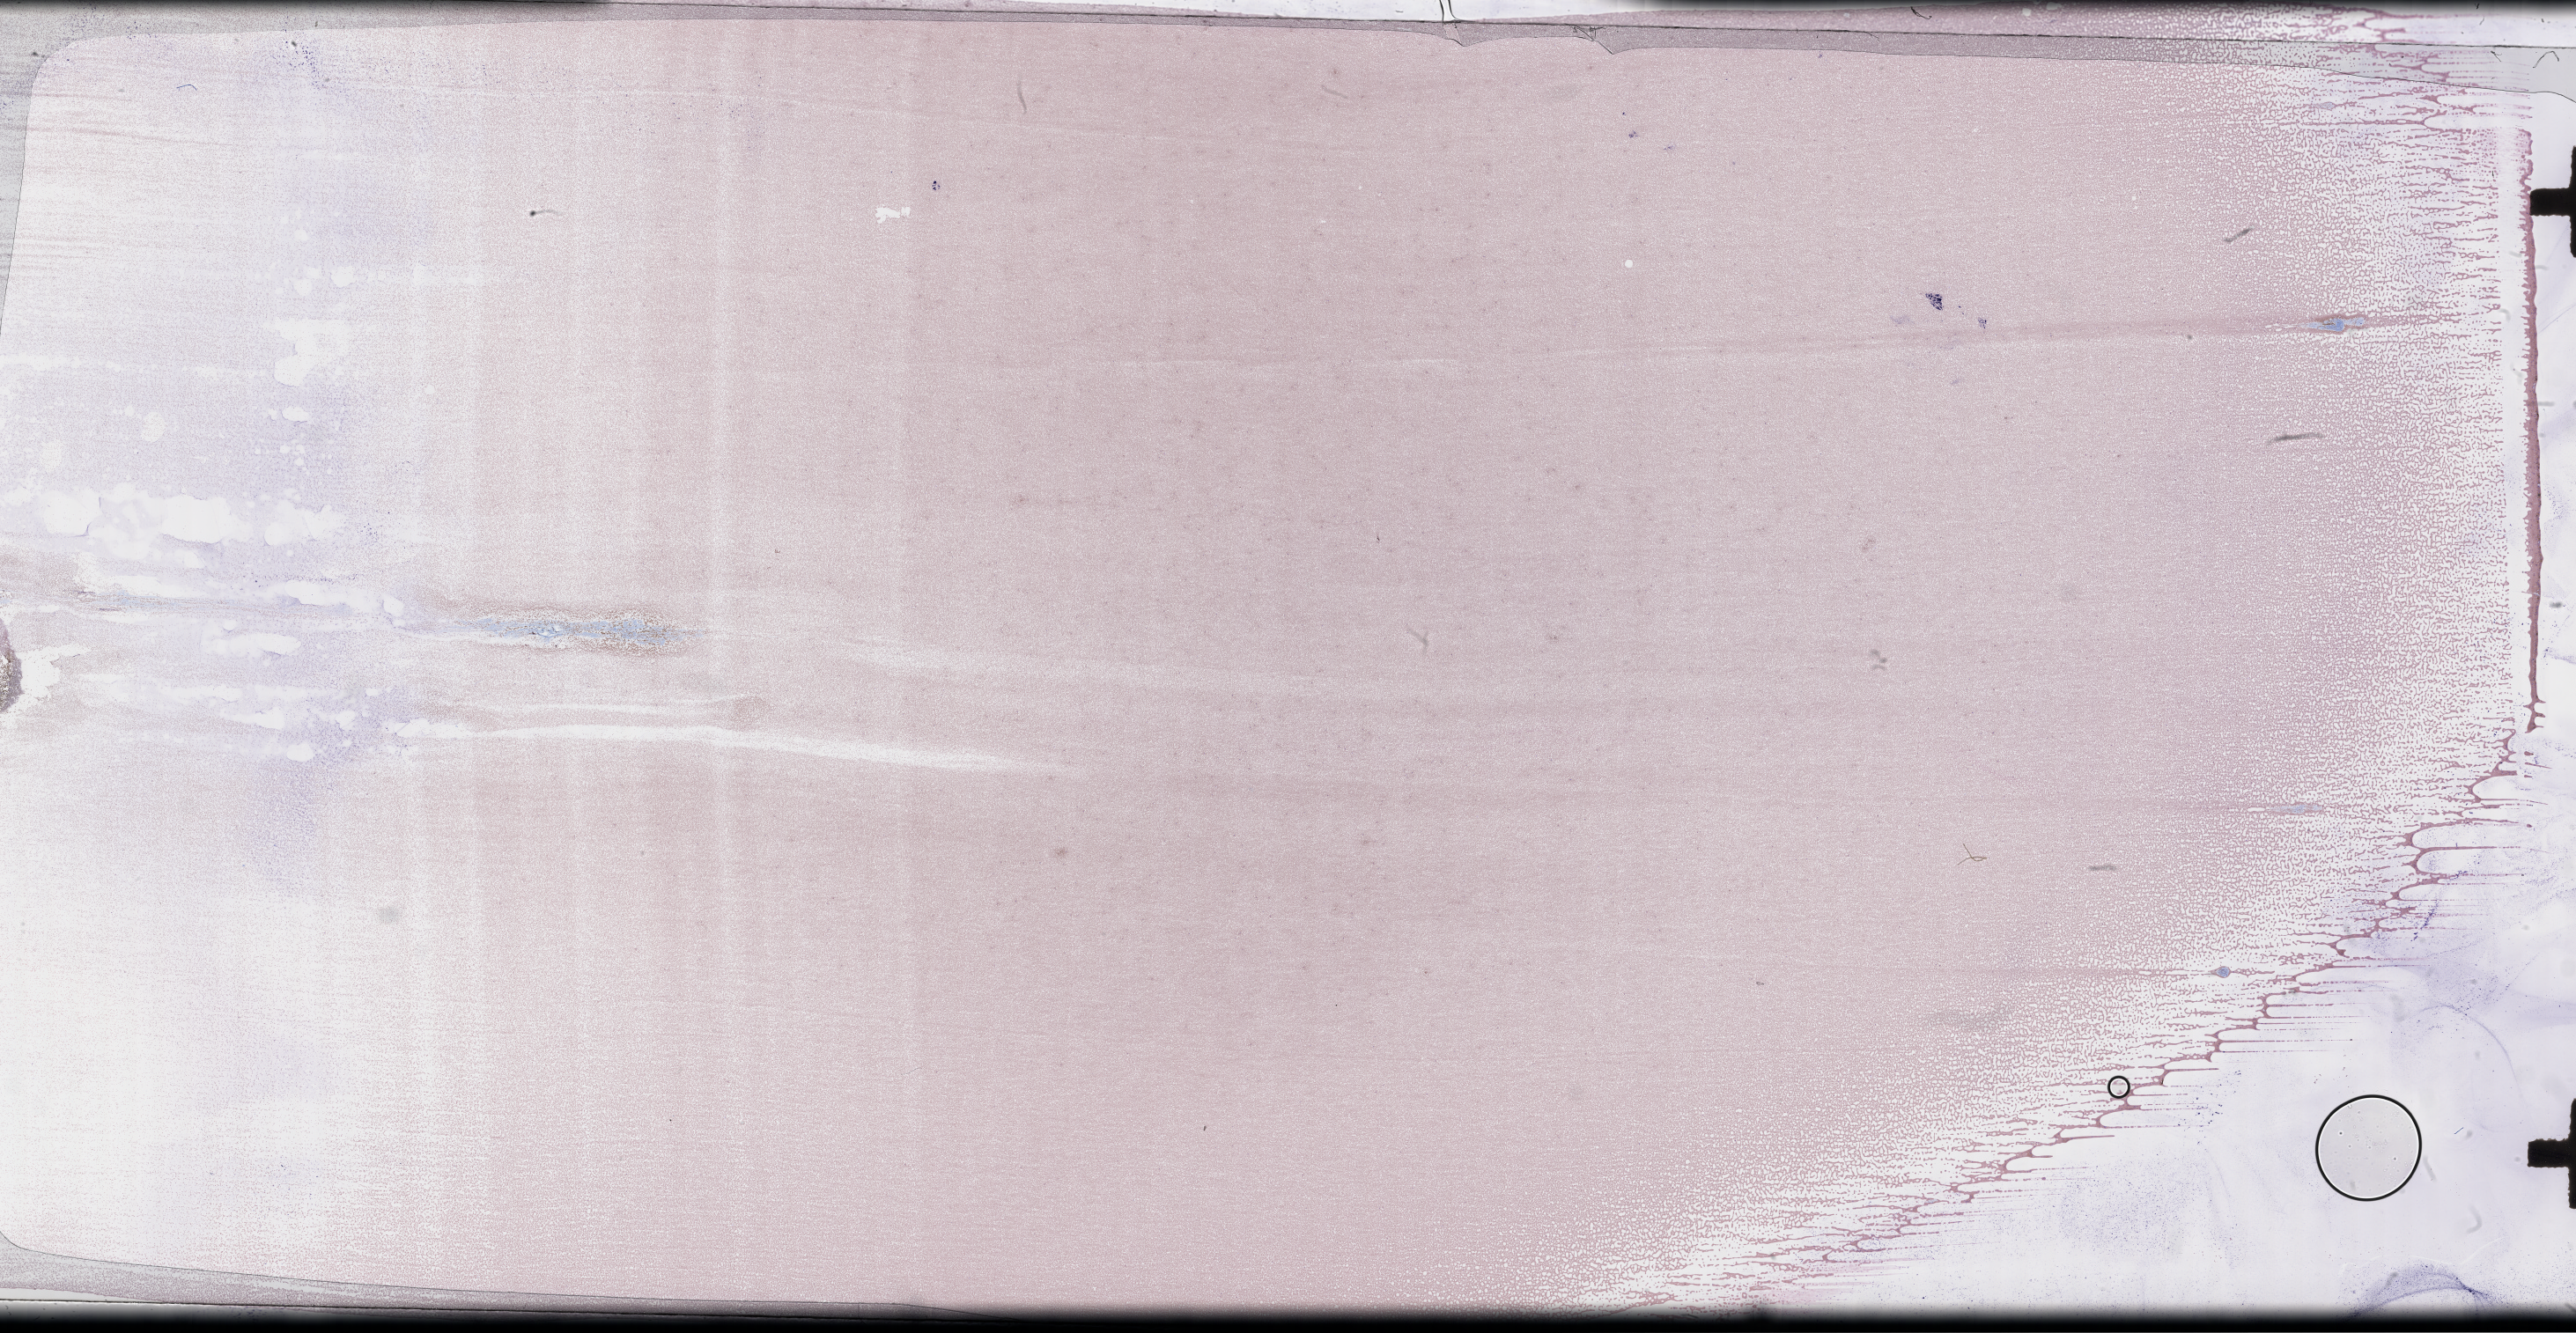
Wright-Giemsa-stained whole blood smear, whole-slide image — shown as a low-resolution overview of the whole scanned area (about 47.2 x 24.5 mm), smear from an EDTA sample. Patient sex: male.
From a patient with: Acute Myeloid Leukemia Not Otherwise Specified.